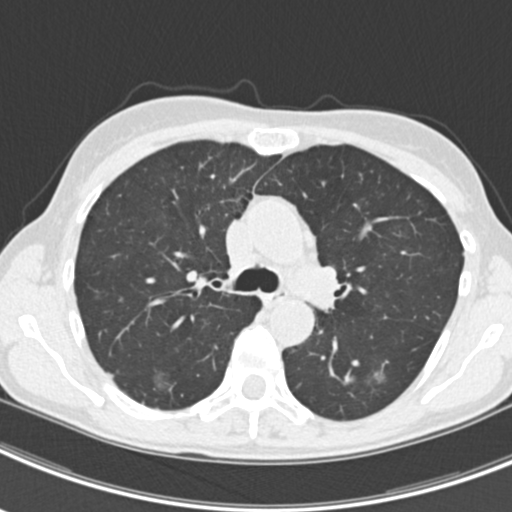
Low-dose screening chest CT, axial slice; second screening round (one year after baseline); lung window (W 1500 / L -600 HU); standard (soft-tissue) reconstruction kernel (B30f); 120 kVp; slice 68 of 219 in the series; 512 × 512 image matrix, field of view 298 × 298 mm. Female participant, aged 63 years at enrolment.
• 2 lesions marked by an expert reader on this slice (largest first), box from (x=143, y=364) to (x=179, y=398) px; (x=365, y=363)–(x=399, y=393).
• The screening reader recorded 9 non-calcified nodules or masses ≥4 mm on this exam; which of them these boxes mark is not recorded.
• Official screen result: positive, other.
• Participant outcome: lung cancer diagnosed 408 days after this screen (after the third annual screen) — bronchiolo-alveolar adenocarcinoma, NOS, right upper lobe, right middle lobe, right lower lobe, left upper lobe, left lower lobe, moderately differentiated (G2), stage IV (AJCC 6th edition).